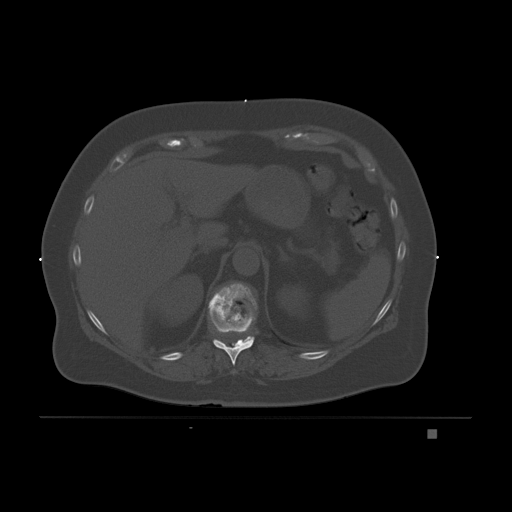
CT including the spine, one axial slice. Slice 96 of 221 in the series (ordered by position). Bone window (W 1800 / L 400 HU). 3 mm slice thickness. 512 × 512 image matrix, field of view 474 × 474 mm. Female patient, age 63 years. From the clinical record (not read from this slice): primary cancer: breast.
Outlined on this slice (semi-automatic segmentation, software-assisted and operator-edited):
- T10 vertebra: box from (x=213, y=331) to (x=253, y=365) px
- T11 vertebra: (x=208, y=283)–(x=257, y=346)